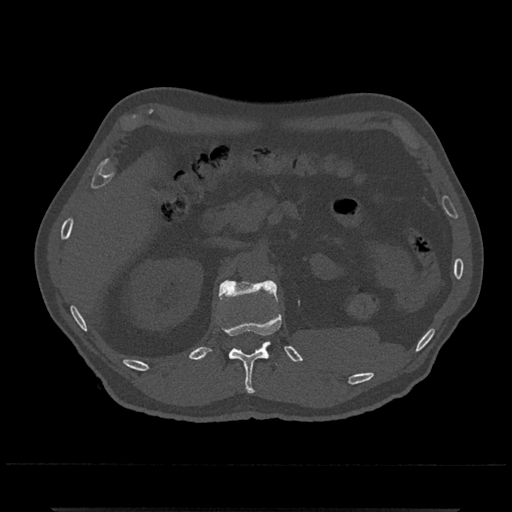
CT including the spine, one axial slice. Position 409 of 797 along the scan axis. Reconstruction kernel Br40s/3. Bone window (W 1800 / L 400 HU). 0.5 mm slice thickness. 512 × 512 image matrix, field of view 393 × 393 mm. Male patient, age 67 years. Case-level facts recorded for this patient, not image findings: primary cancer: prostate.
Structures marked on this image (semi-automatic segmentation, software-assisted and operator-edited):
- L1 vertebra: bounding box <219,280,278,358> (left, top, right, bottom; pixels)
- T12 vertebra: <222,315,282,394>